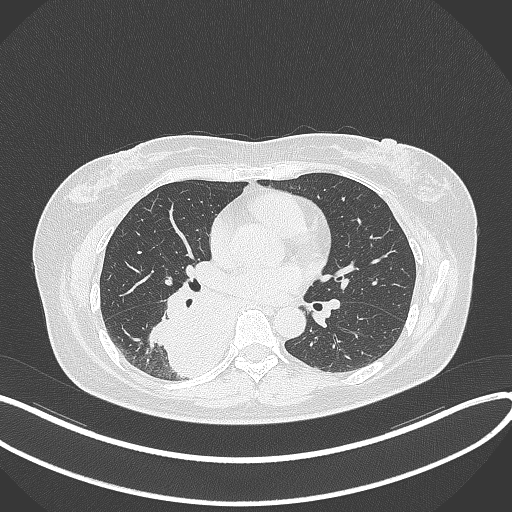
Chest CT, one axial slice. Position 180 of 331 along the scan axis. Reconstruction kernel B70f. 120 kVp. Lung window (W 1500 / L -600 HU). 1 mm slice thickness. 512 × 512 image matrix. Female patient, age 54 years. Case-level facts recorded for this patient, not image findings: clinical TNM (as recorded): T4 N0 M0.
Outlined on this slice (bounding box drawn by a radiologist):
- lung tumour (recorded histology: adenocarcinoma): box from (x=142, y=284) to (x=230, y=378) px